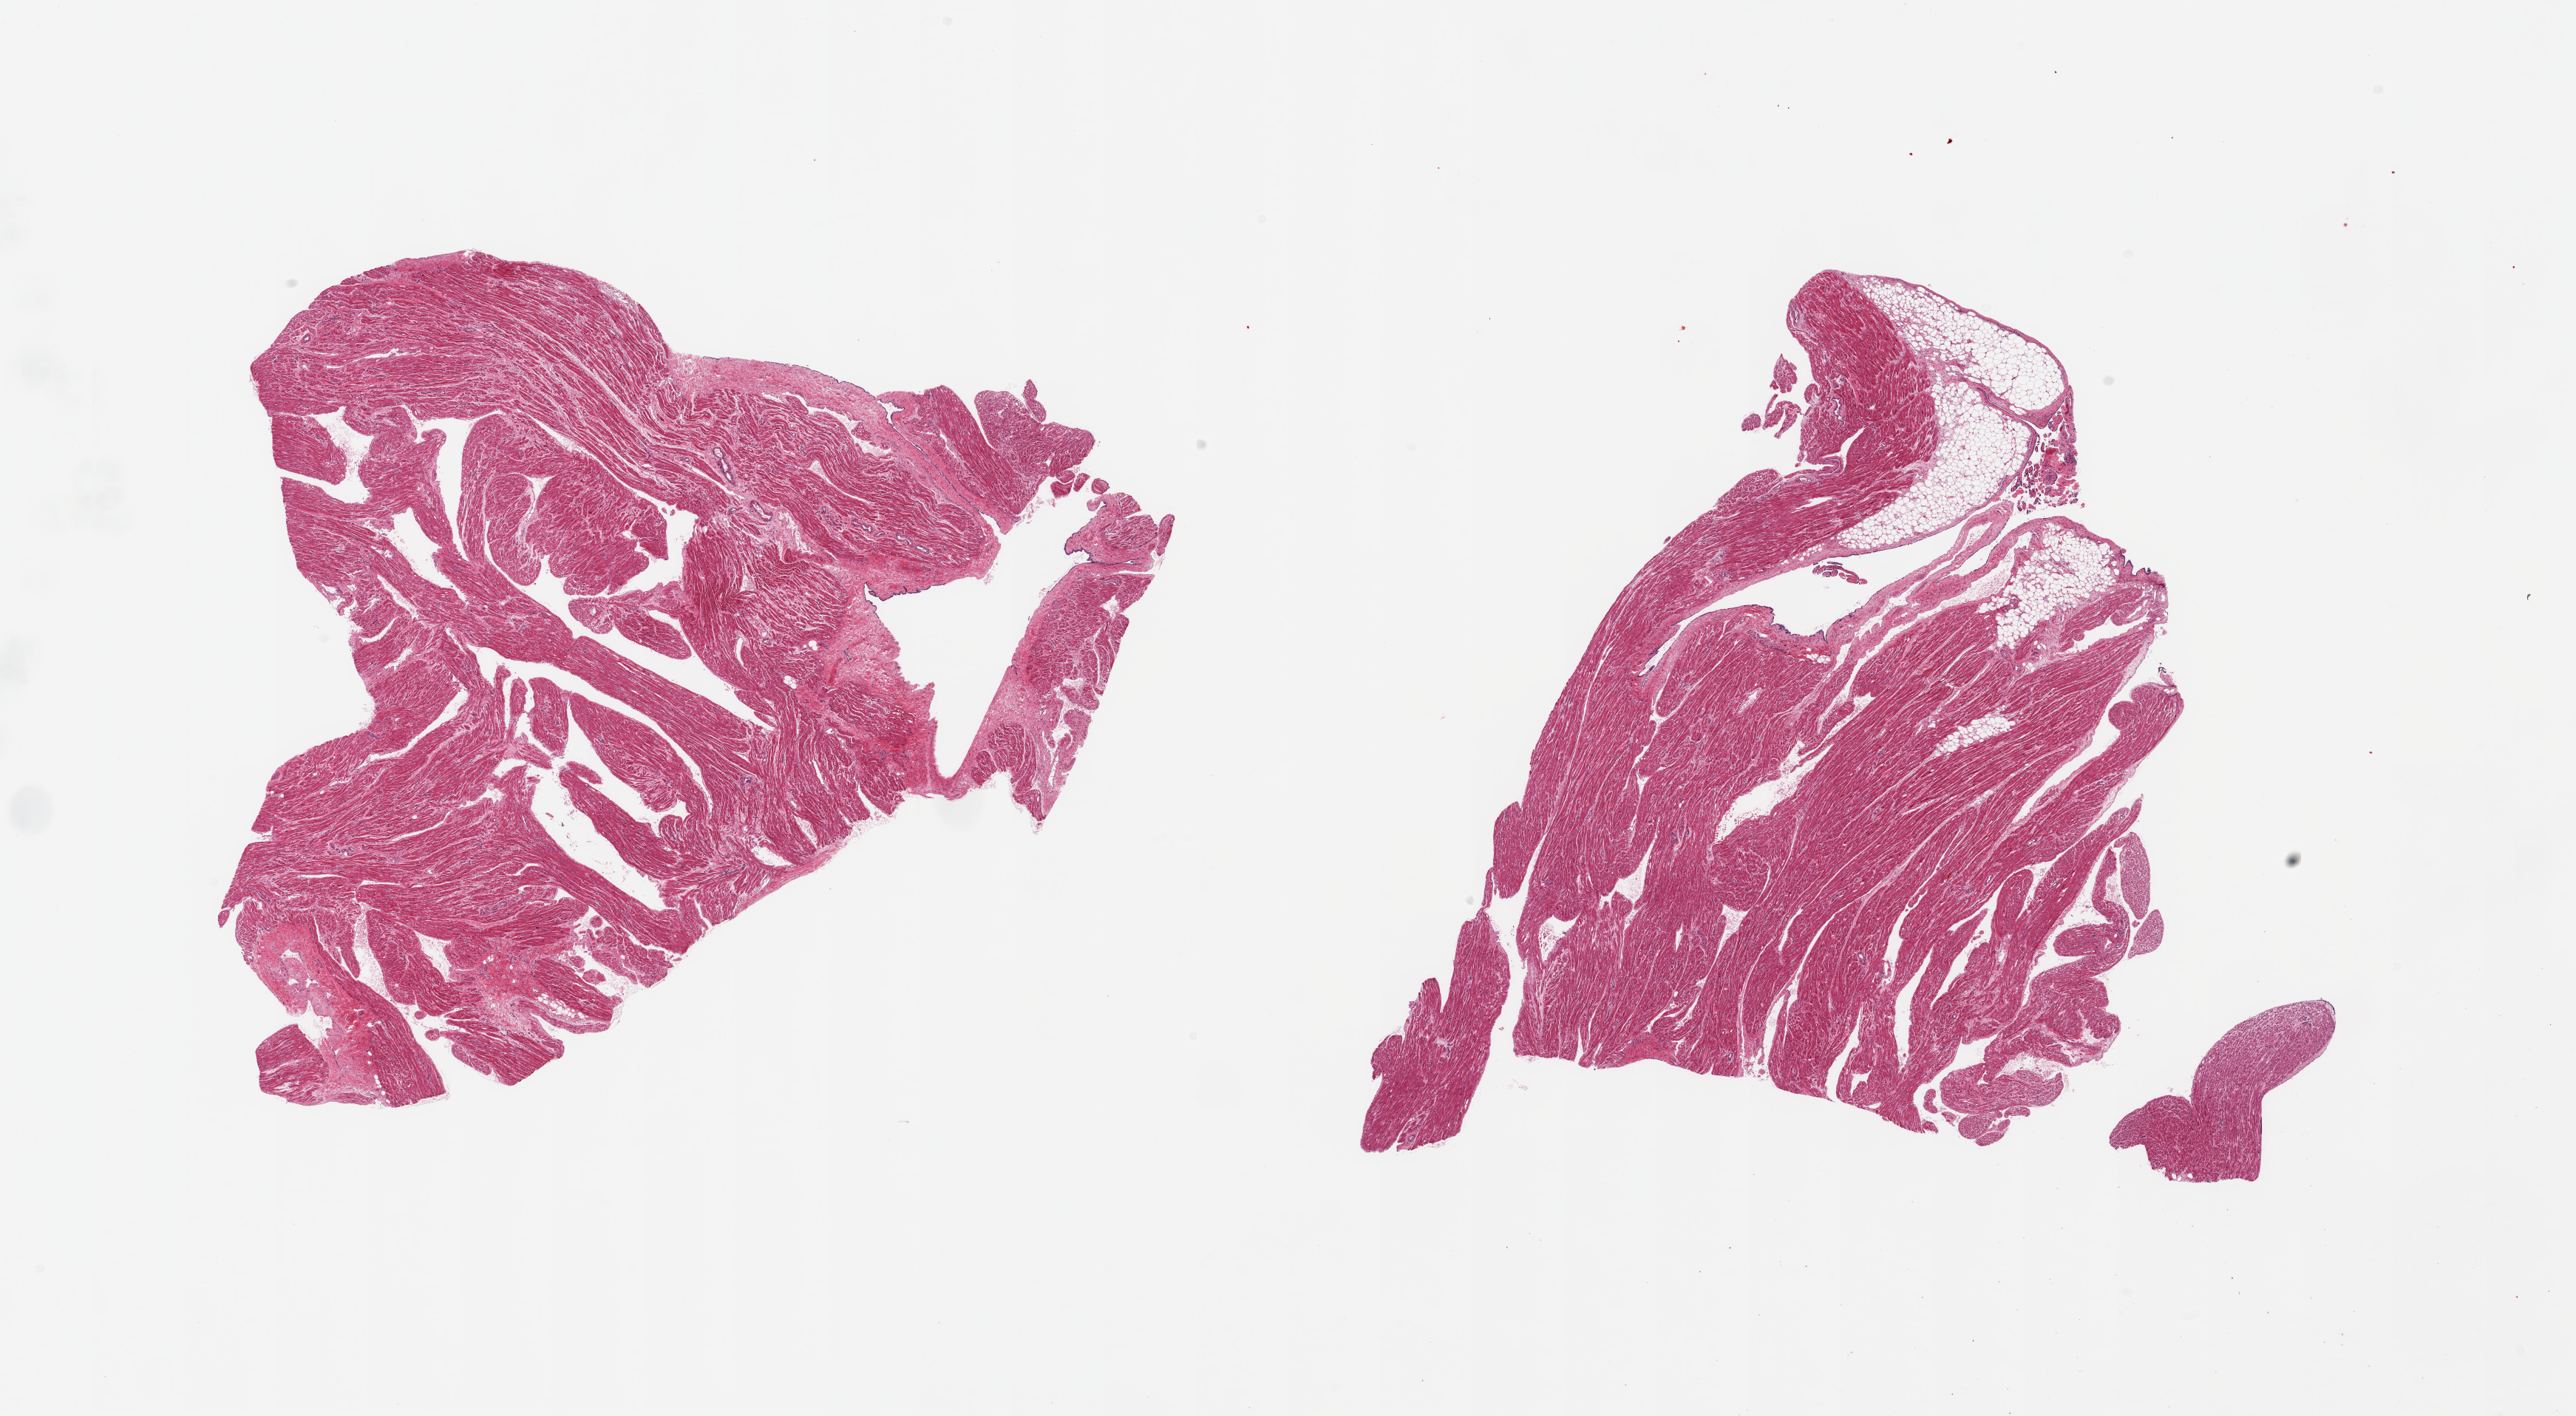
H&E whole-slide image, brightfield — whole scanned area (about 27.6 x 15.2 mm, acquisition: 20x scan) shown as a low-resolution overview, PAXgene-fixed paraffin-embedded (PFPE) section, sampled site (target tissue): auricular appendage, tissue donor sample. Donor: male.
• pathologist's review note for this sample: 2 pieces; one piece includes ~10% fat